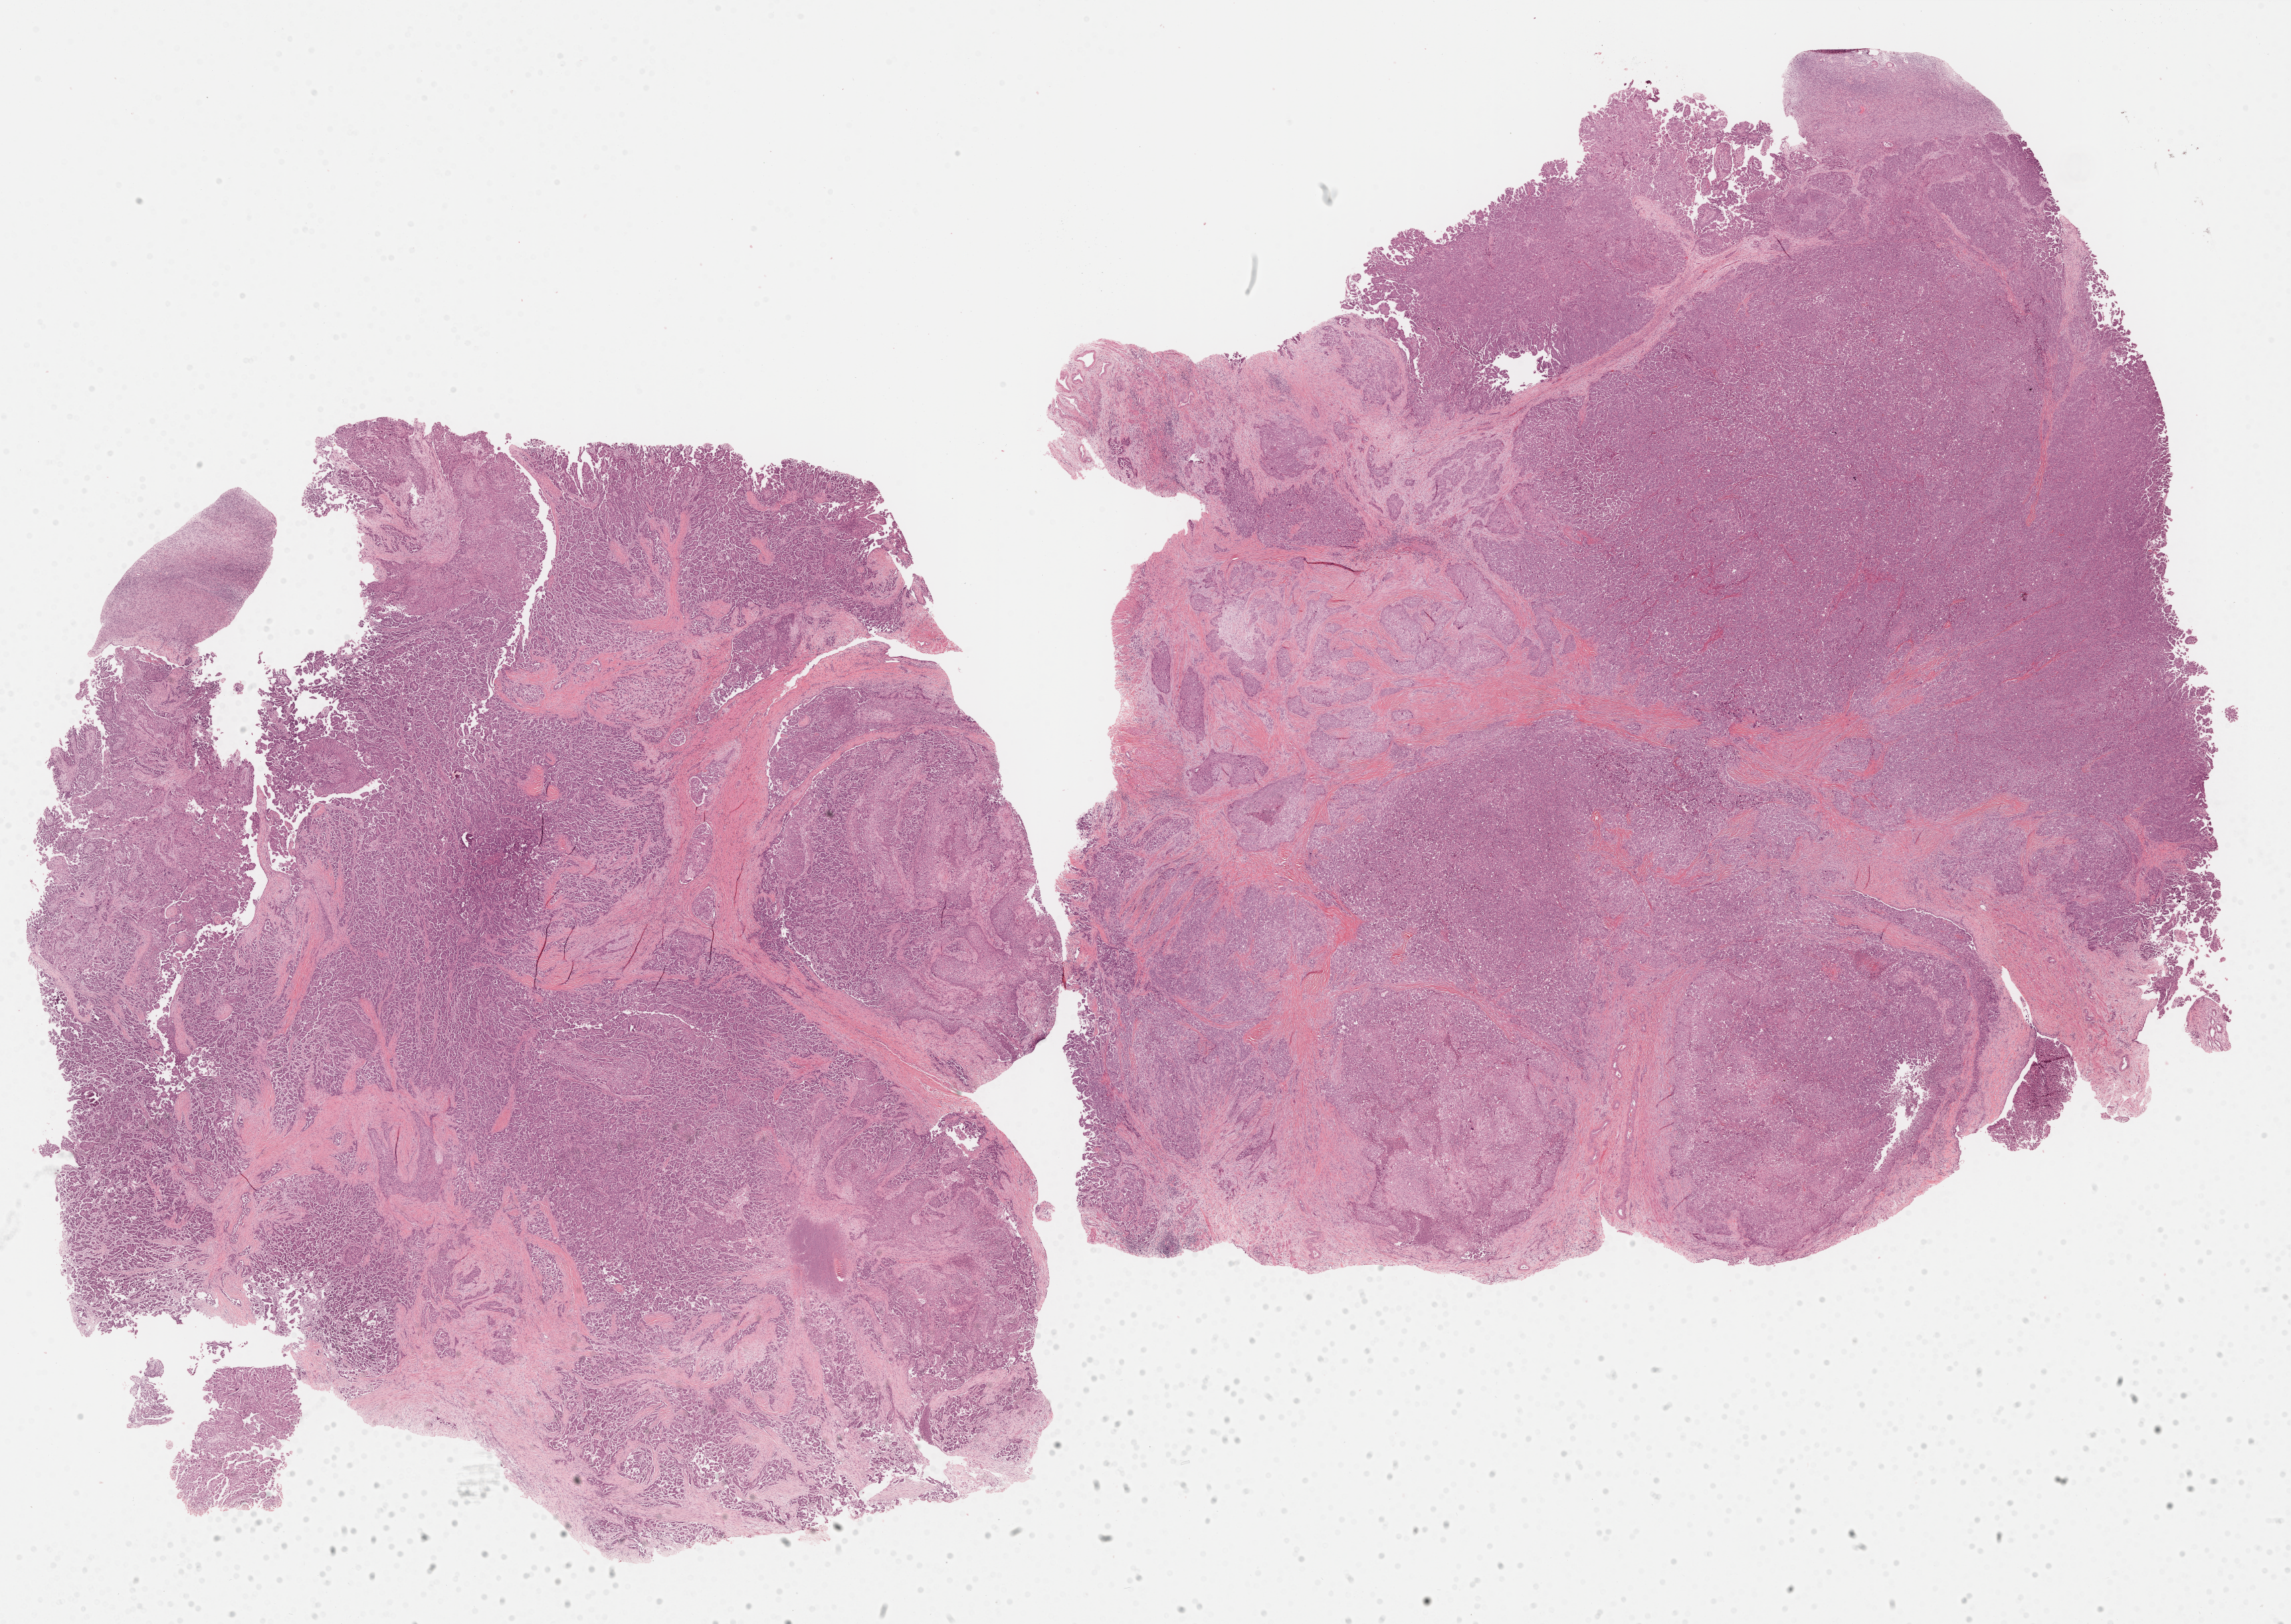
Whole-slide histology image, Hematoxylin and eosin (H&E) stained — shown as a low-resolution overview of the whole scanned area (about 27.7 x 19.6 mm), formalin-fixed paraffin-embedded (FFPE) diagnostic section, primary tumour sample from the ovary. Patient: female, age at initial diagnosis 71 years. Histologic grade: G3 (poorly differentiated).
Histologic diagnosis: Serous cystadenocarcinoma, NOS. FIGO stage: IV.